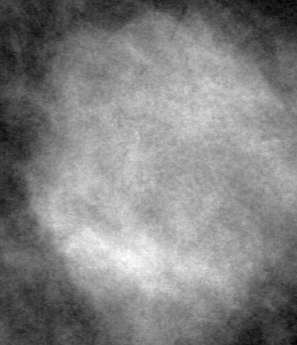
Cropped region of a digitized screen-film mammogram centred on a radiologist-marked abnormality; right breast; MLO view.
Marked abnormality: mass, shape lobulated, margins ill defined; BI-RADS assessment category 4; subtlety rating 2 on a 1 (subtle) to 5 (obvious) scale; pathology result (as recorded, not read from the image): benign.